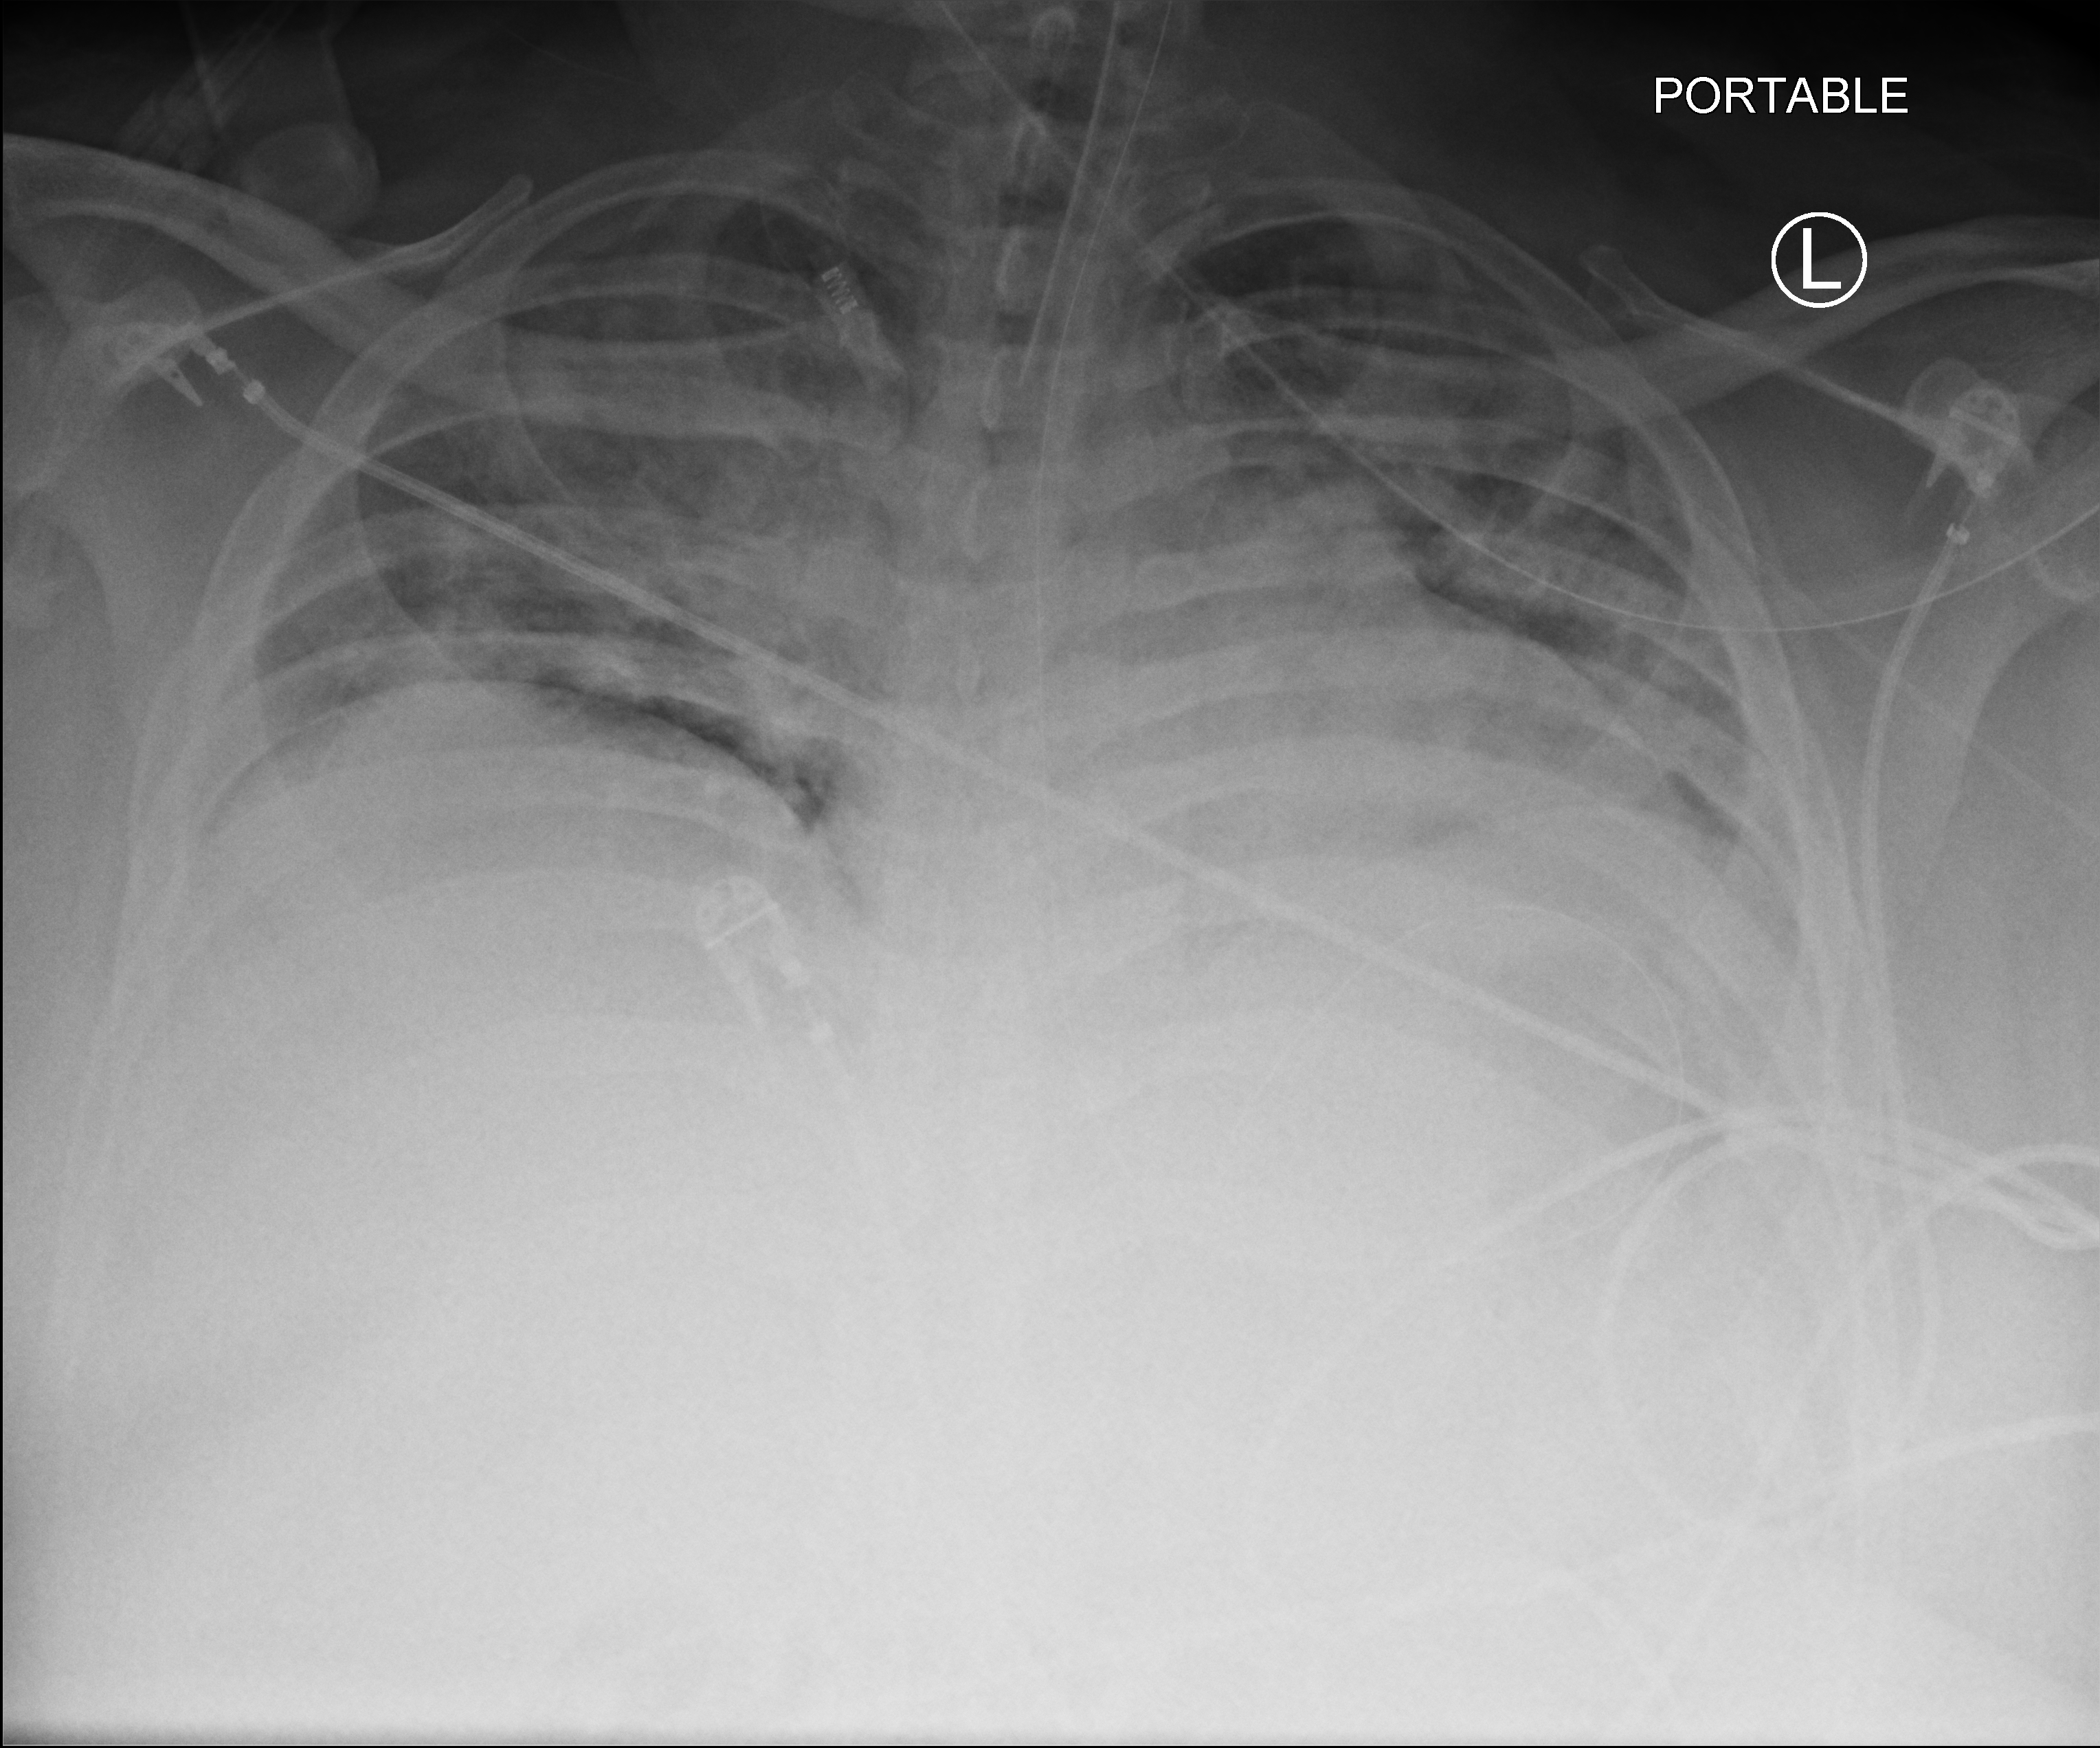
Portable chest radiograph; anteroposterior (AP) projection. Male patient hospitalised with COVID-19, age 18–59 years.
Admission-level facts for this patient (not findings on this image; timing relative to this image not recorded):
- admitted to intensive care during this hospital stay: yes
- mechanically ventilated during this hospital stay: yes
- length of hospital stay: 69 days